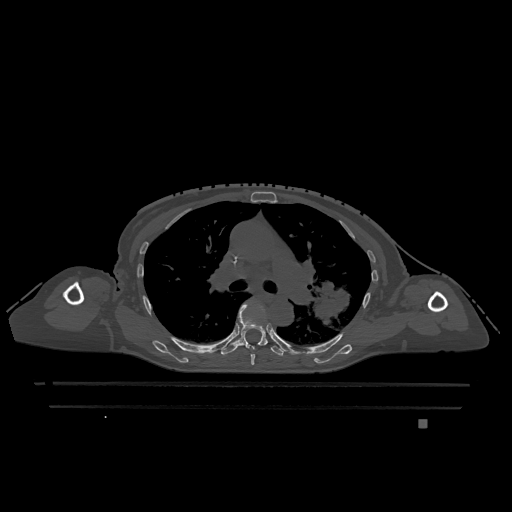
CT including the spine, one axial slice; slice 807 of 1317 in the series (ordered by position); bone window (W 1800 / L 400 HU); 0.5 mm slice thickness; 512 × 512 image matrix. Patient: female, 74 years. From the clinical record (not read from this slice): primary cancer: lung; vertebrae with lytic lesions (as recorded): T1, T4, T5, T6, L4, L5.
Outlined on this slice (semi-automatically segmented with operator editing):
- T5 vertebra: bounding box (x1, y1, x2, y2) in pixels: (251, 354, 255, 365)
- T6 vertebra: (221, 304, 284, 356)